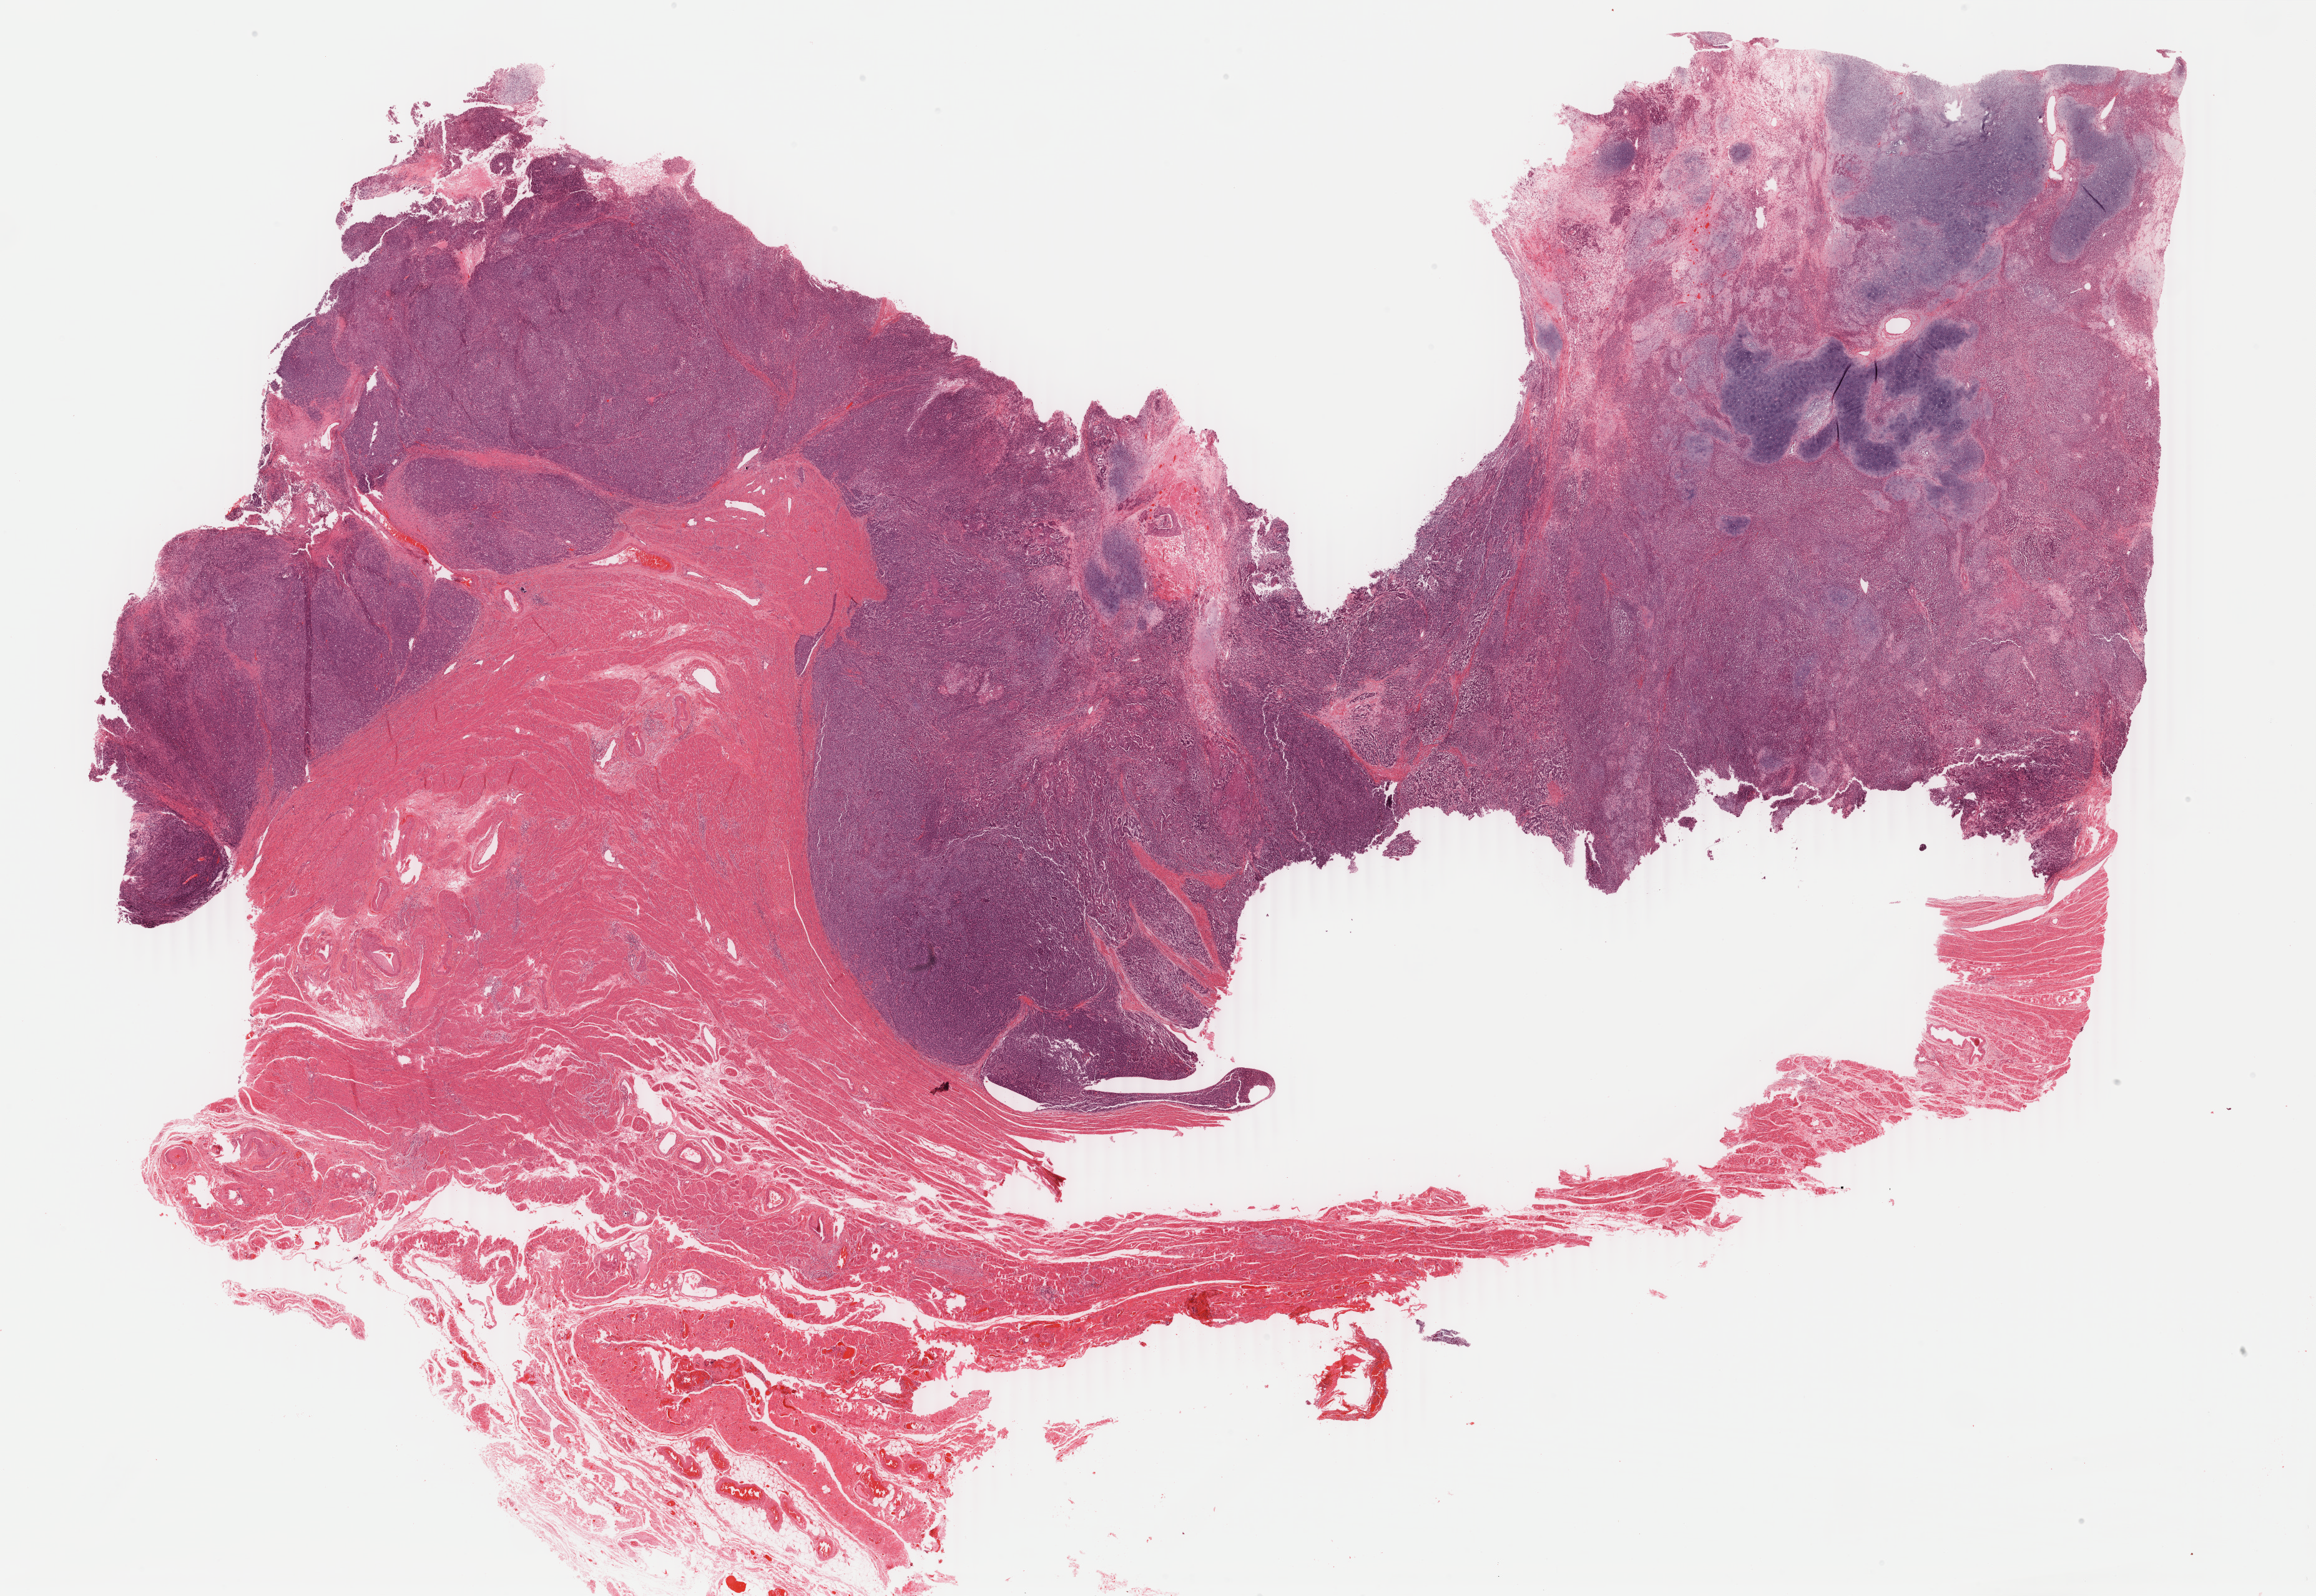
Whole-slide histology image, H&E-stained, a low-resolution overview of the entire scanned area, about 29.5 x 20.3 mm (acquisition: 40x scan). Formalin-fixed paraffin-embedded (FFPE) diagnostic section. Sample: primary tumour, uterus. Female patient; age at initial diagnosis 65 years.
Diagnosis: Mullerian mixed tumor (endometrium). FIGO stage: IIIC.